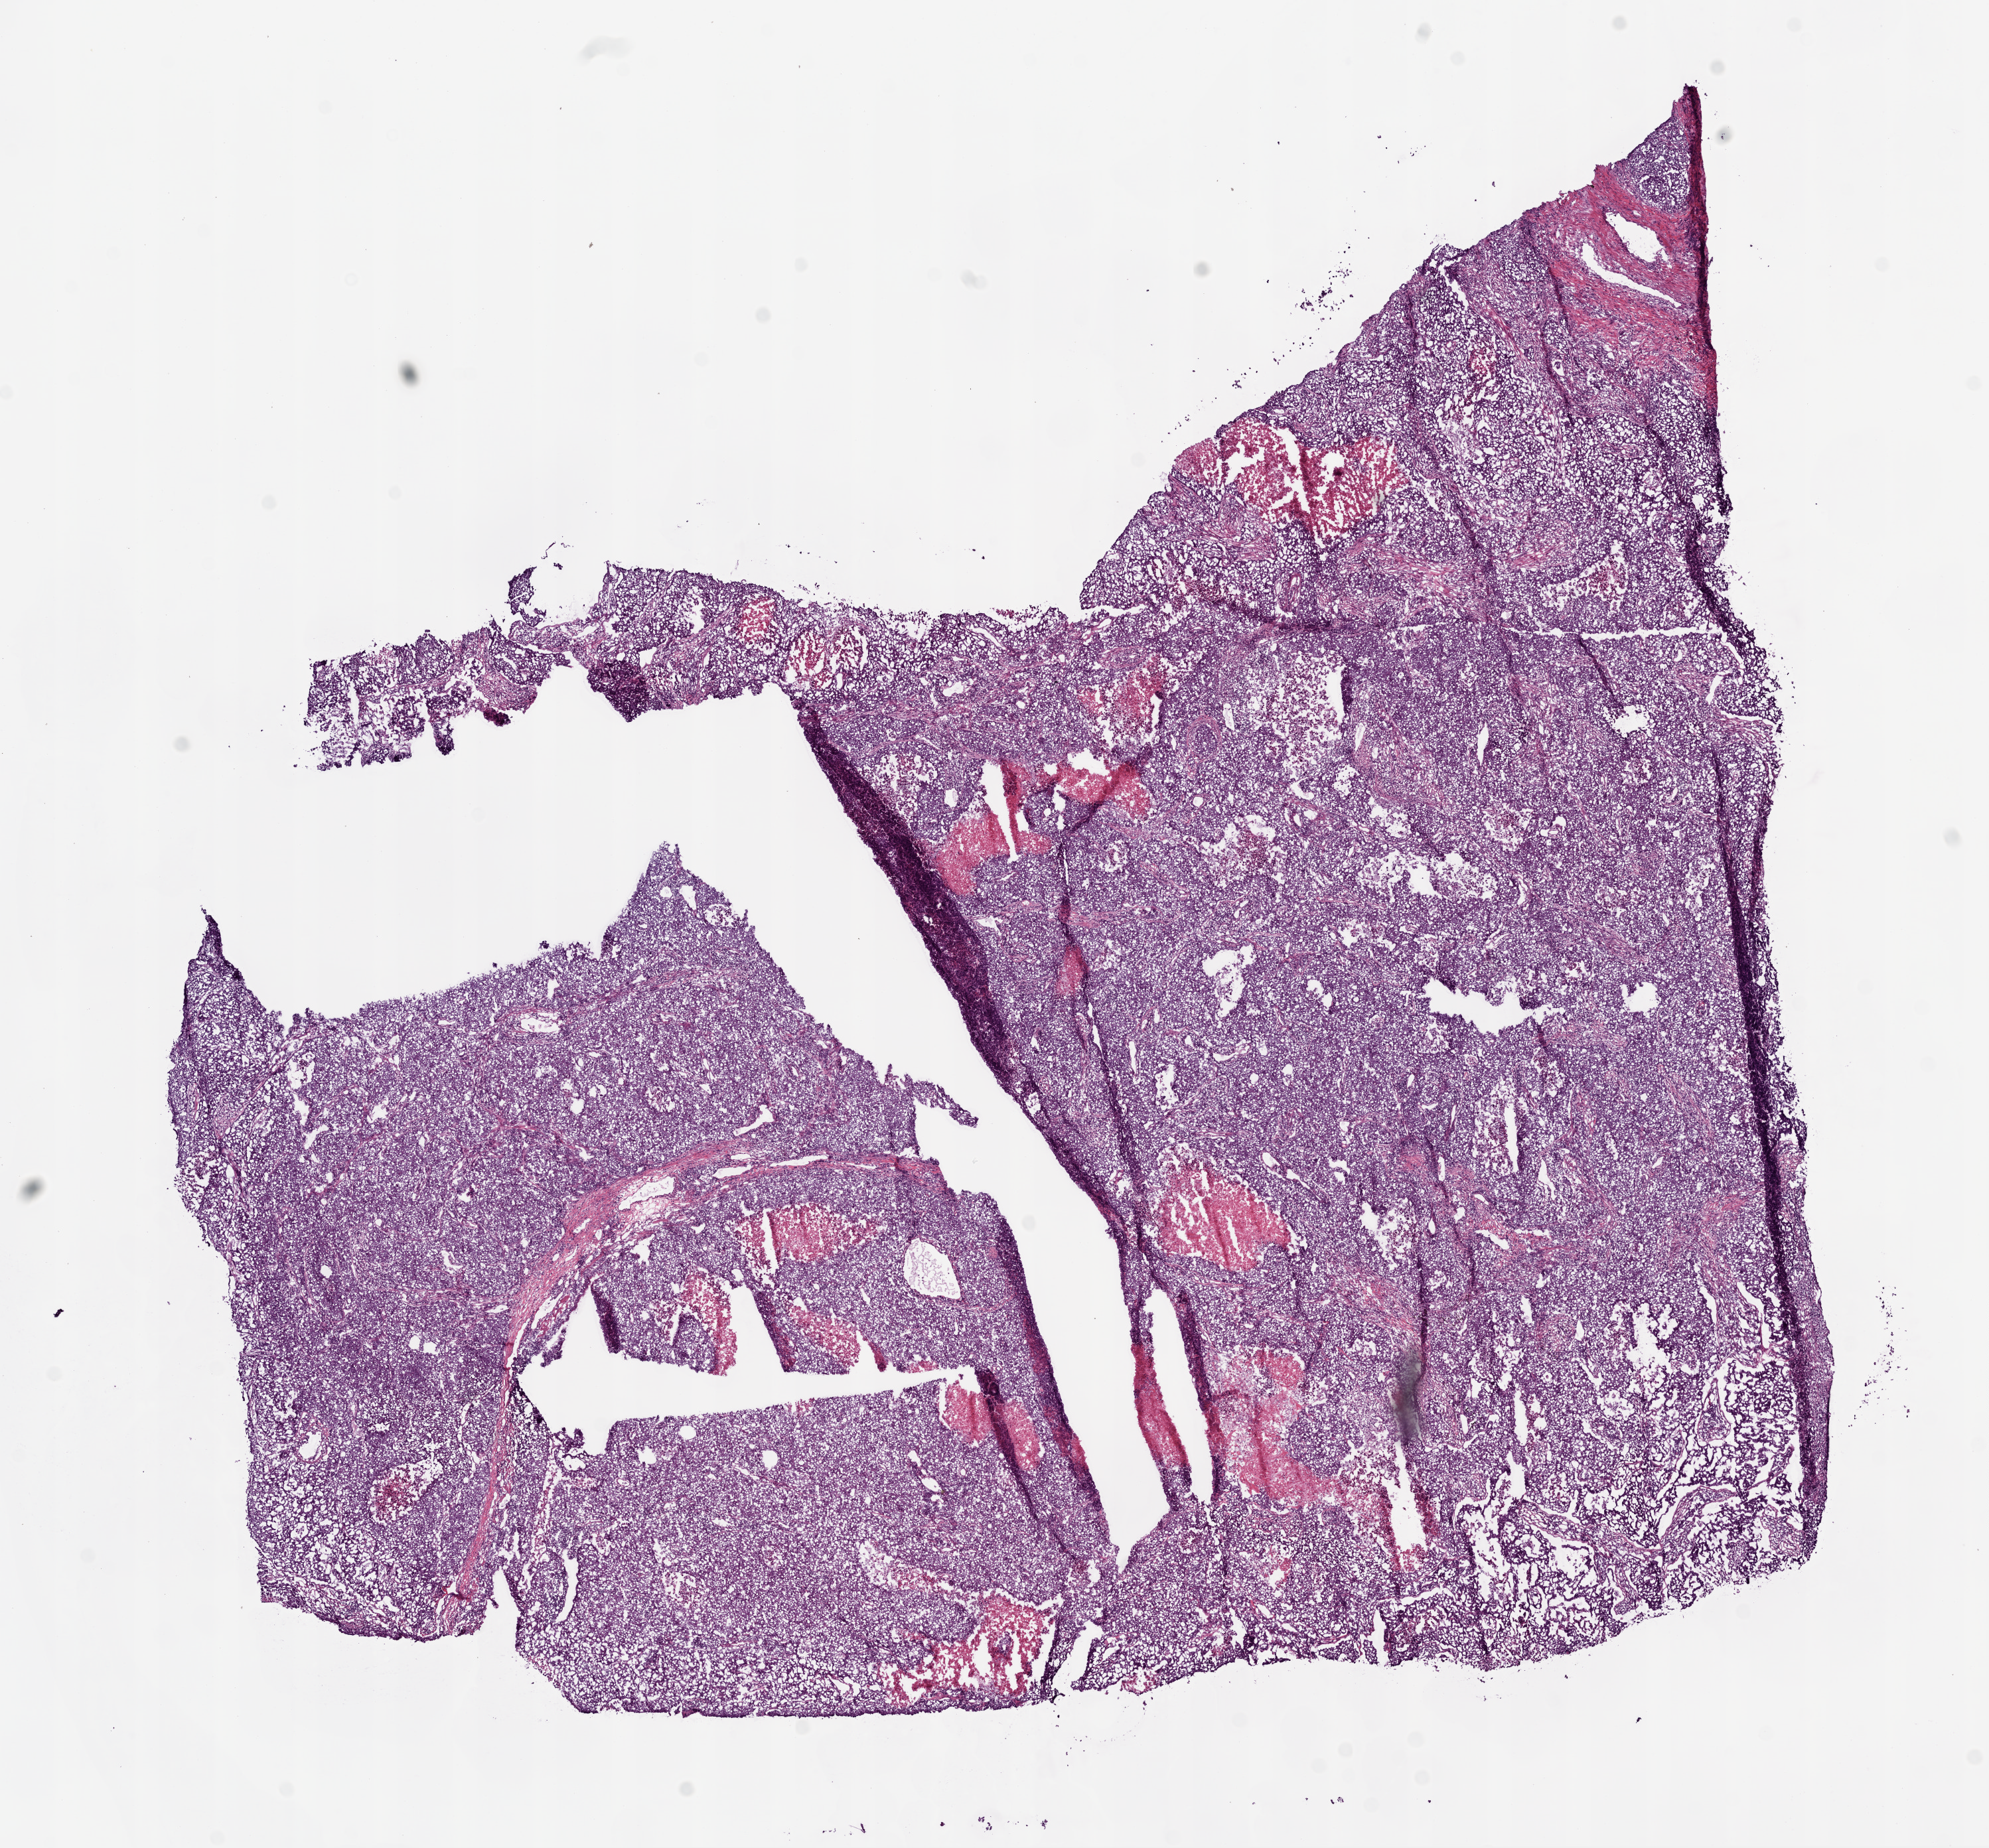
Digitized H&E tissue section (whole slide), whole scanned area (about 12.1 x 11.2 mm, acquisition: 20x scan) shown as a low-resolution overview; frozen section from the bottom of the tissue portion; primary tumour sample from the lung. Male, age 64 years at initial diagnosis. Composition of this section per pathologist review: tumour cells 76%, tumour nuclei 75%, normal cells 0%, stromal cells 12%, necrosis 12%.
- TNM: T2 N2 M0
- laterality: right
- histologic diagnosis: Squamous cell carcinoma, NOS
- AJCC pathologic stage: IIIA (7th edition)